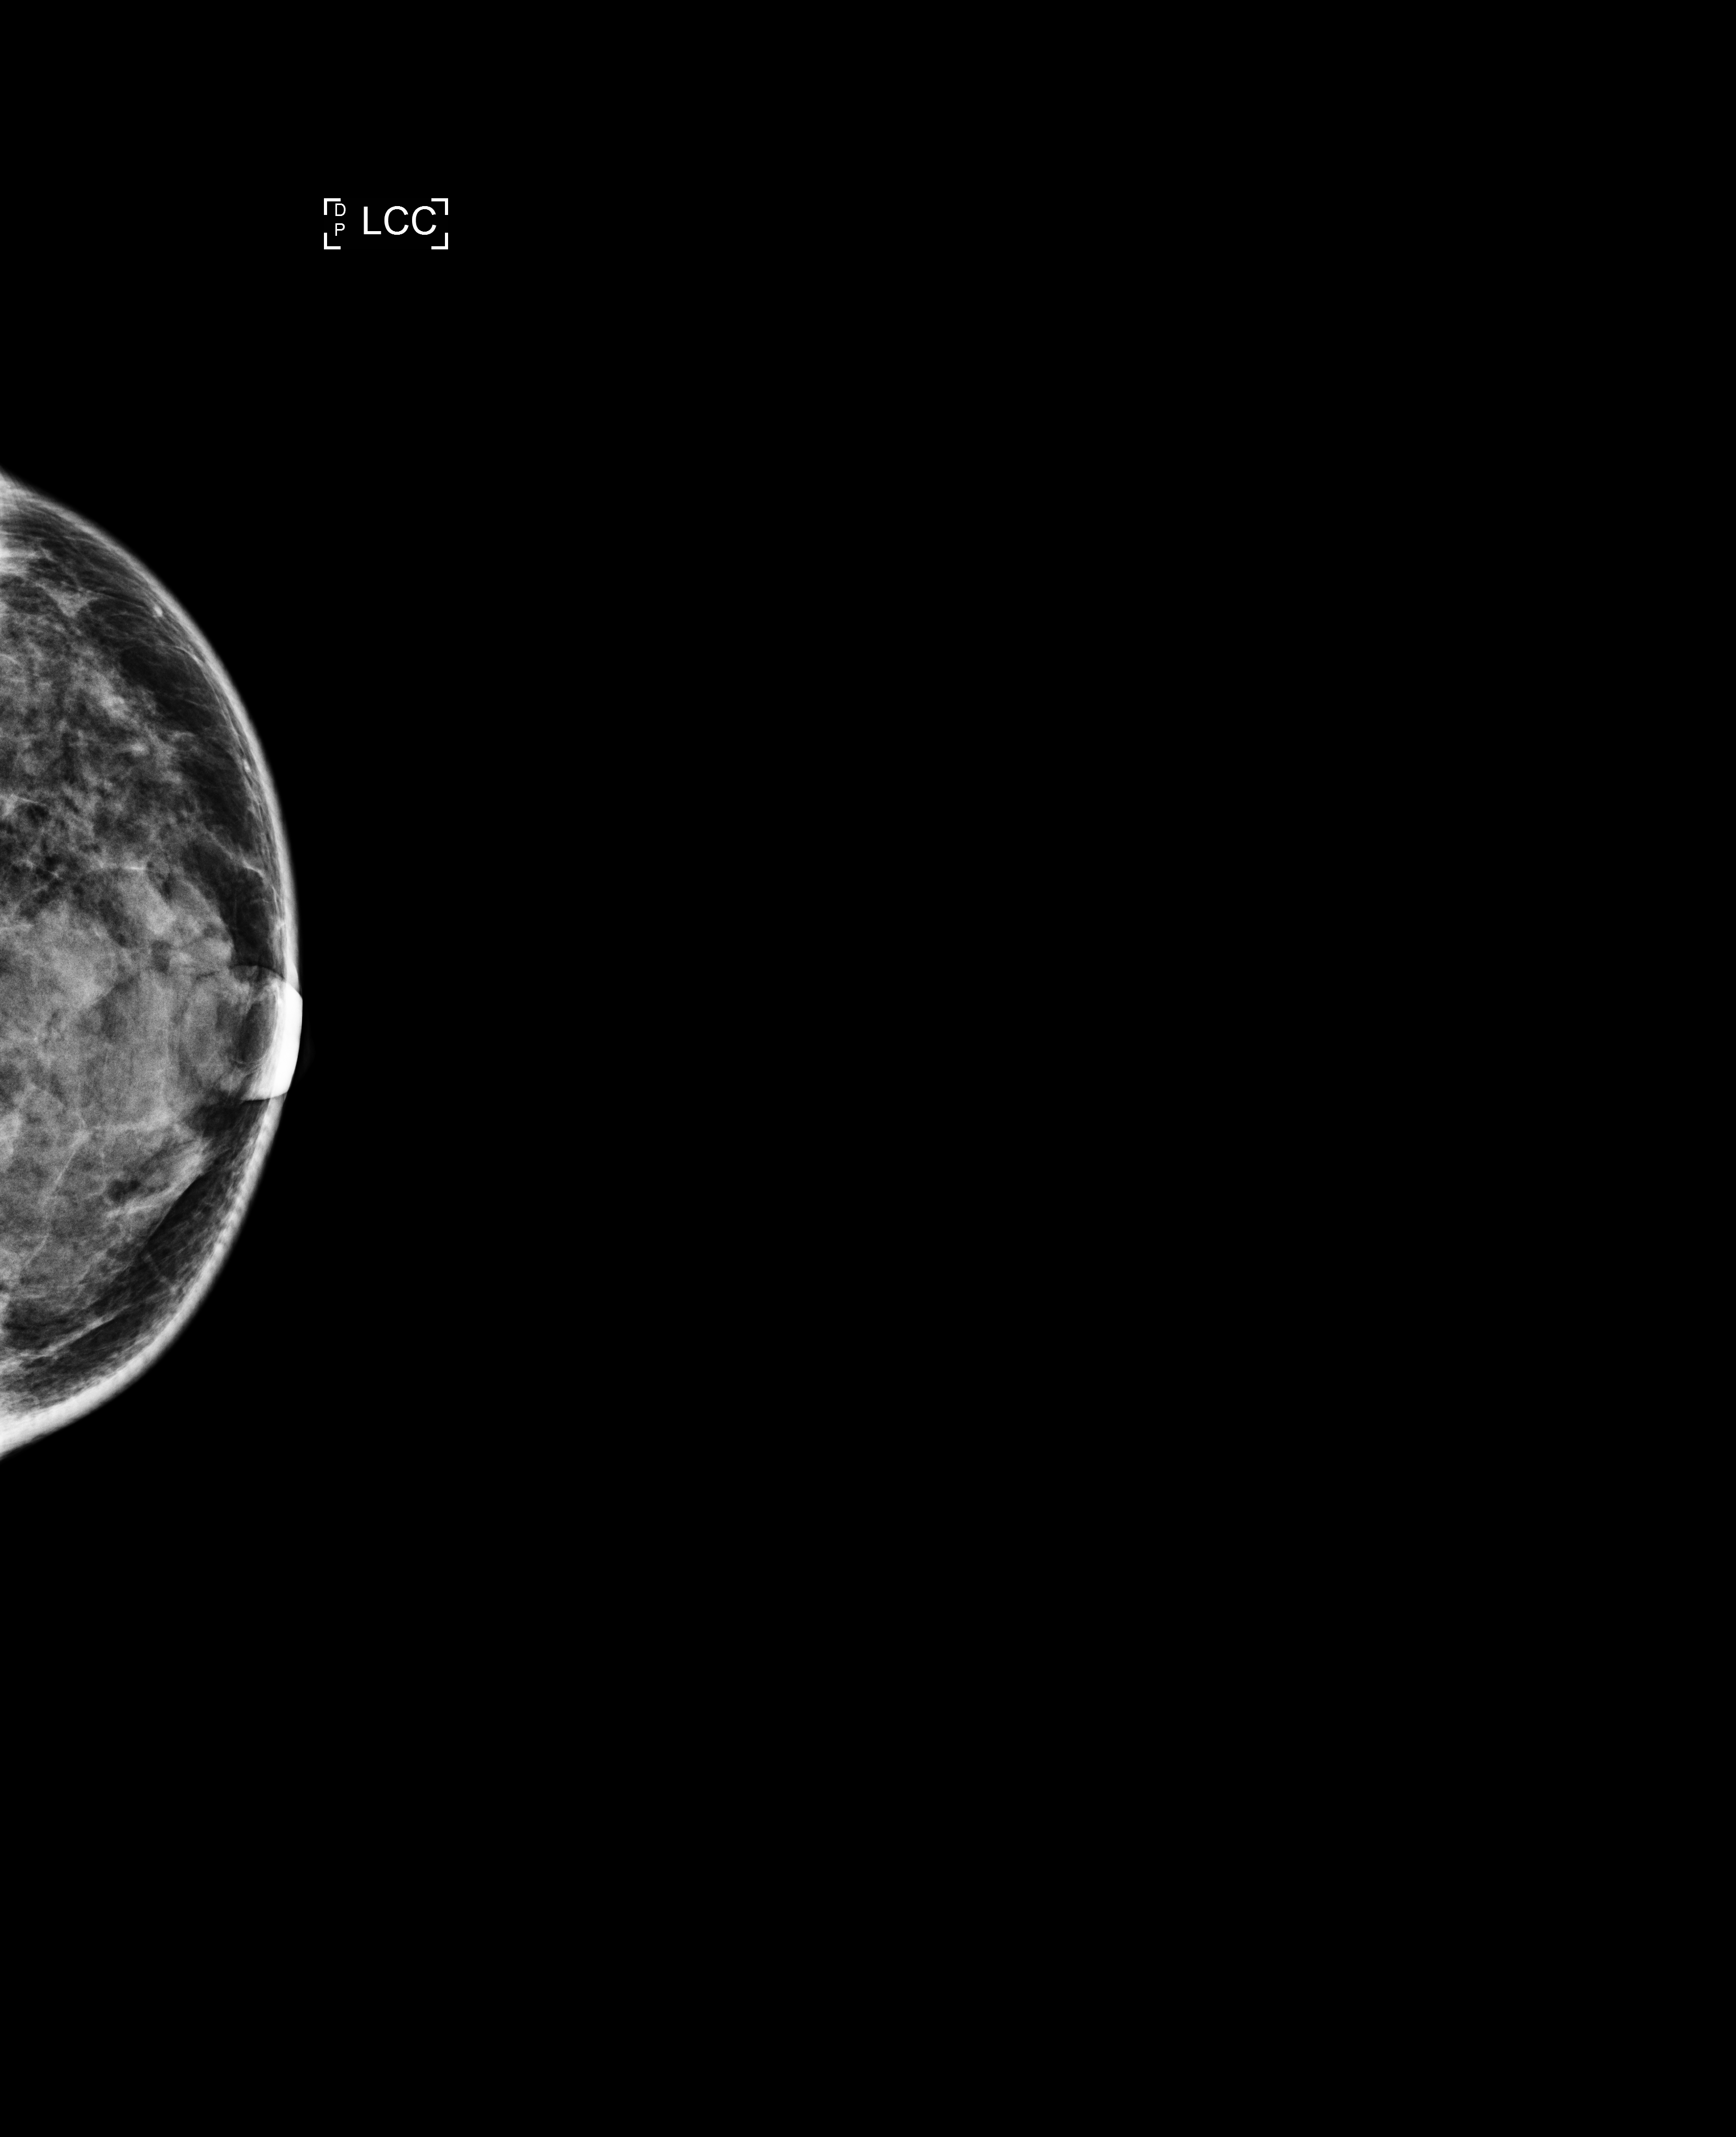
Screening examination. Female patient, age 60 years.
Image type: full-field digital mammogram. Breast: left. Projection: CC view.